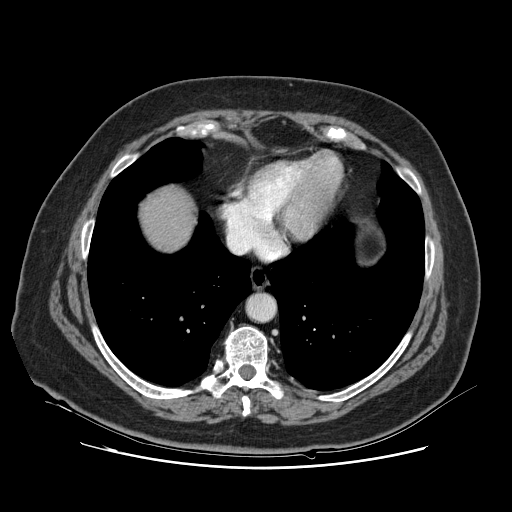
Contrast-enhanced abdominal CT, one axial slice; slice 119 of 132 in the series (ordered by position); soft-tissue window (W 400 / L 40 HU); 512 × 512 image matrix, field of view 391 × 391 mm. Female patient, age 73 years. From the clinical record (not read from this slice): diagnosis: colorectal cancer liver metastases, imaged before liver resection; multiple liver metastases: no; largest metastasis: 7 cm; disease in both lobes: no.
Structures marked on this image (expert manual segmentation):
- liver: bounding box <141,190,193,251> (left, top, right, bottom; pixels)
- planned liver remnant (the part of the liver to remain after resection): <141,191,193,251>